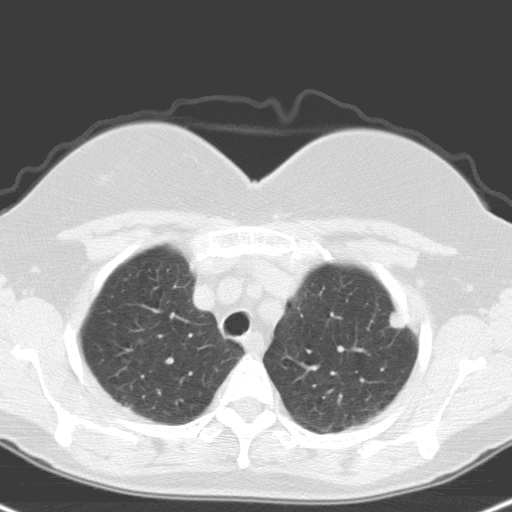
Low-dose screening chest CT, axial slice, baseline screening round, lung window (W 1500 / L -600 HU), standard (soft-tissue) reconstruction kernel (C), slice 22 of 148 in the series, 512 × 512 image matrix, field of view 314 × 314 mm. Female, age 59 years at enrolment.
Lesion marked by an expert reader, bounding box (x1, y1, x2, y2) in pixels: (380, 300, 421, 343). The screening reader recorded 2 non-calcified nodules or masses ≥4 mm on this exam (right upper lobe, left upper lobe); which of them this box marks is not recorded. Participant outcome: lung cancer diagnosed 48 days after this screen — large cell neuroendocrine carcinoma, left upper lobe, poorly differentiated (G3), stage IA (AJCC 6th edition), 12 mm at pathology.